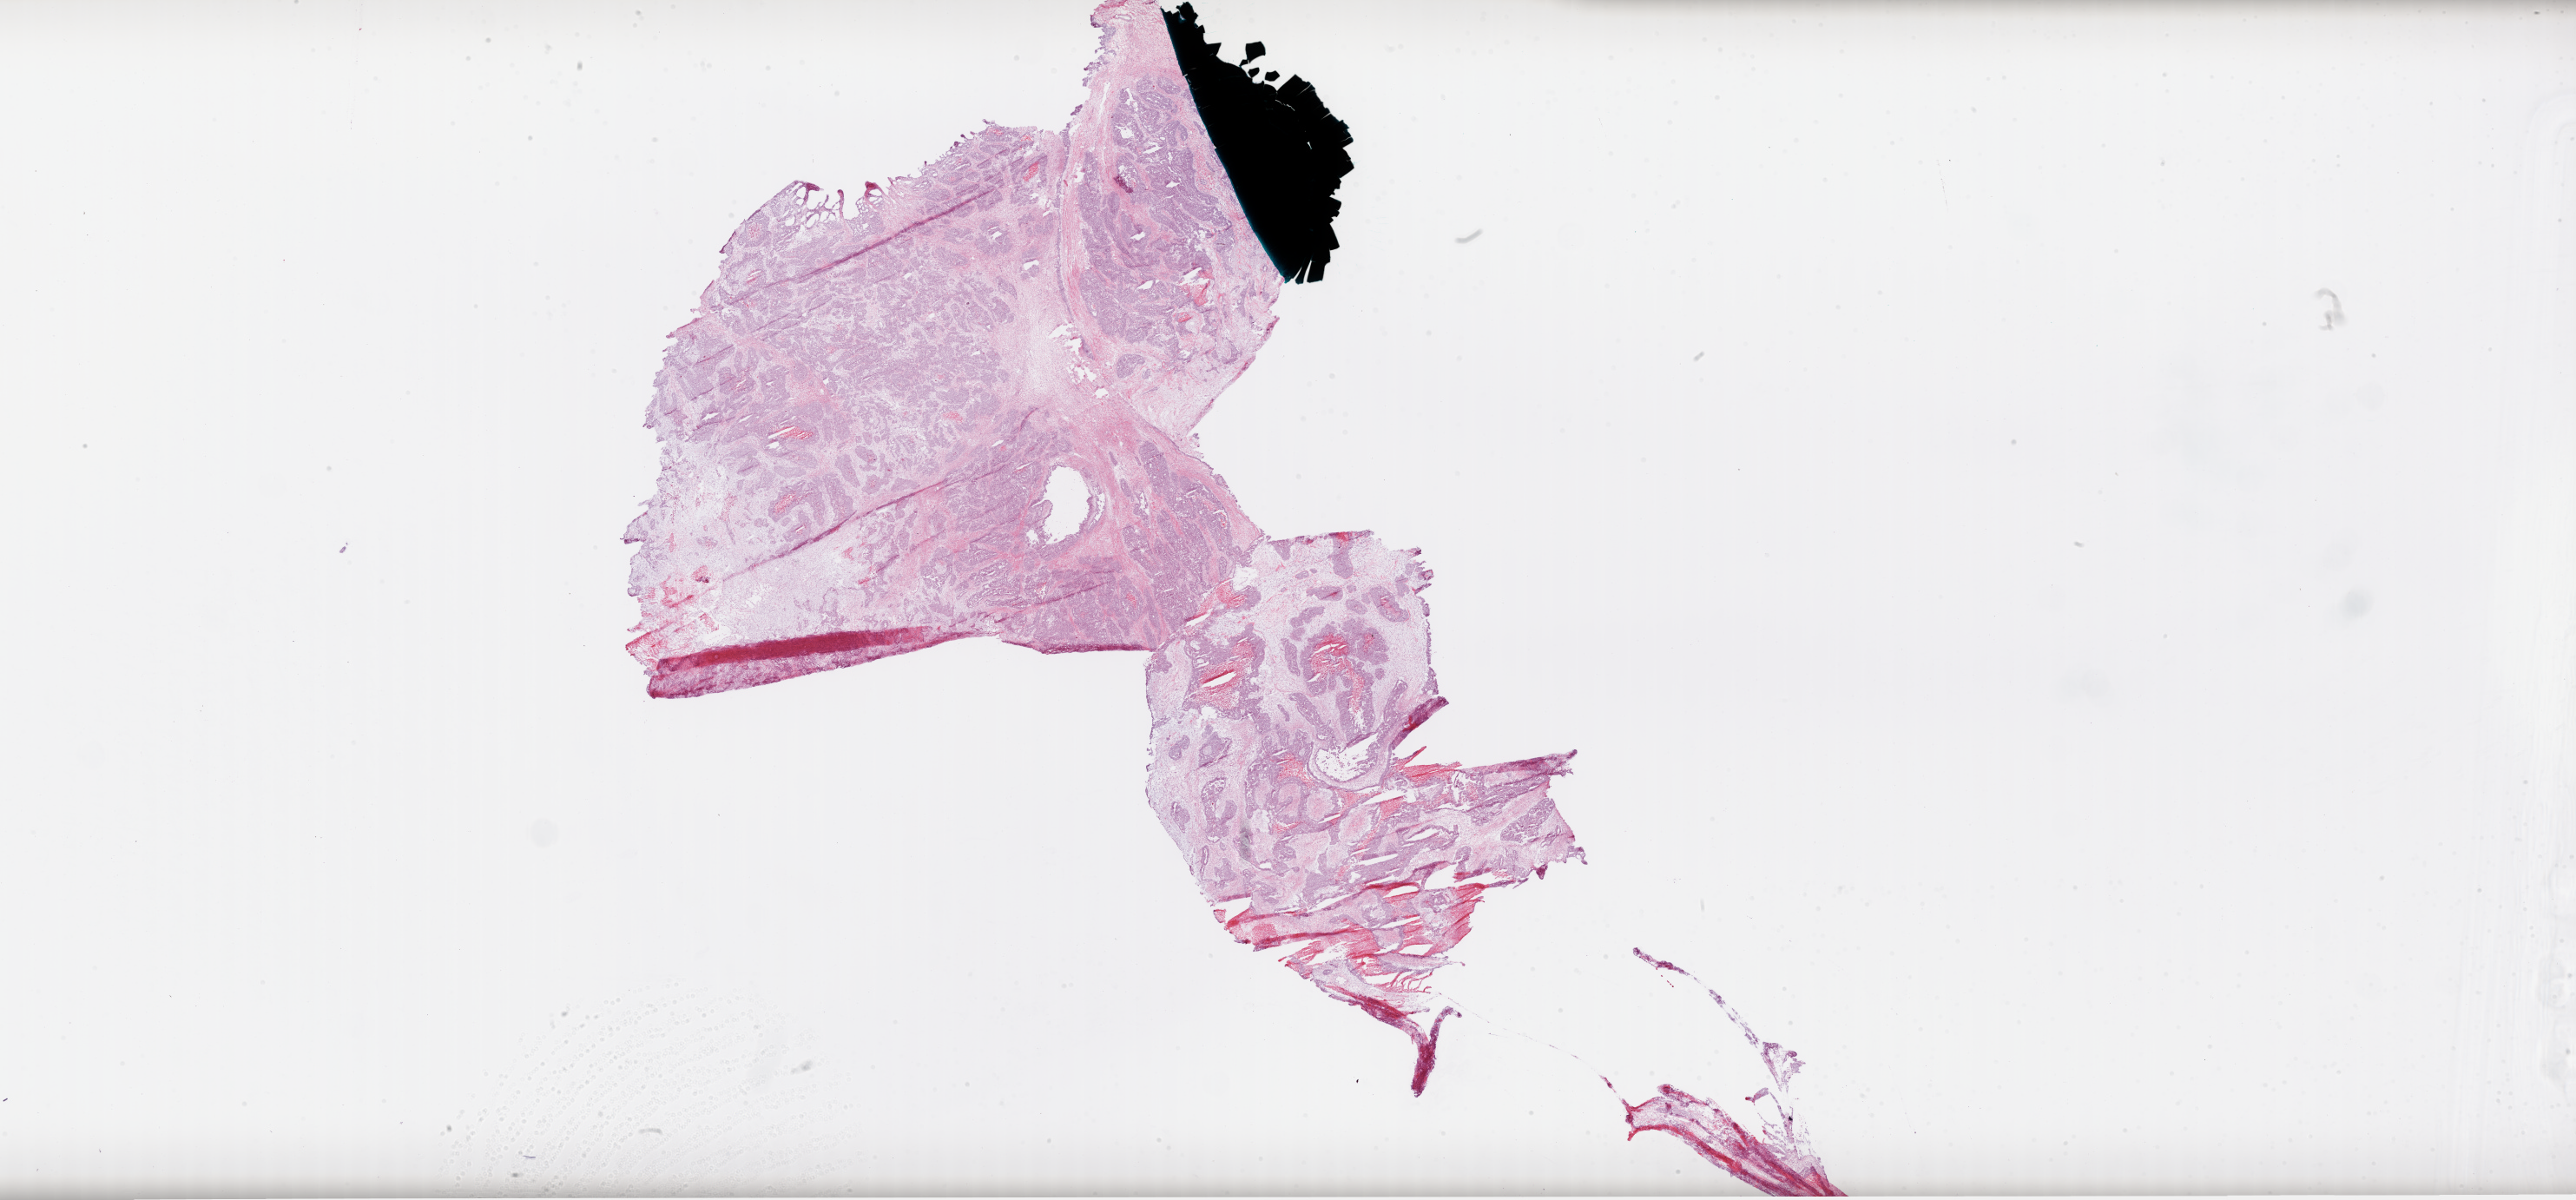
Whole-slide histology image, H&E — whole scanned area (about 47.9 x 22.3 mm, acquisition: 20x scan) shown as a low-resolution overview; frozen section from the bottom of the tissue portion; sample: primary tumour, ovary. Female, age 72 years at initial diagnosis. Histologic grade: G3 (poorly differentiated). Slide review estimates, as recorded: tumour cells 65%, tumour nuclei 75%, normal cells 0%, stromal cells 25%, necrosis 10%.
FIGO stage: IIIC. Laterality: bilateral. Pathologic diagnosis: Serous cystadenocarcinoma, NOS.